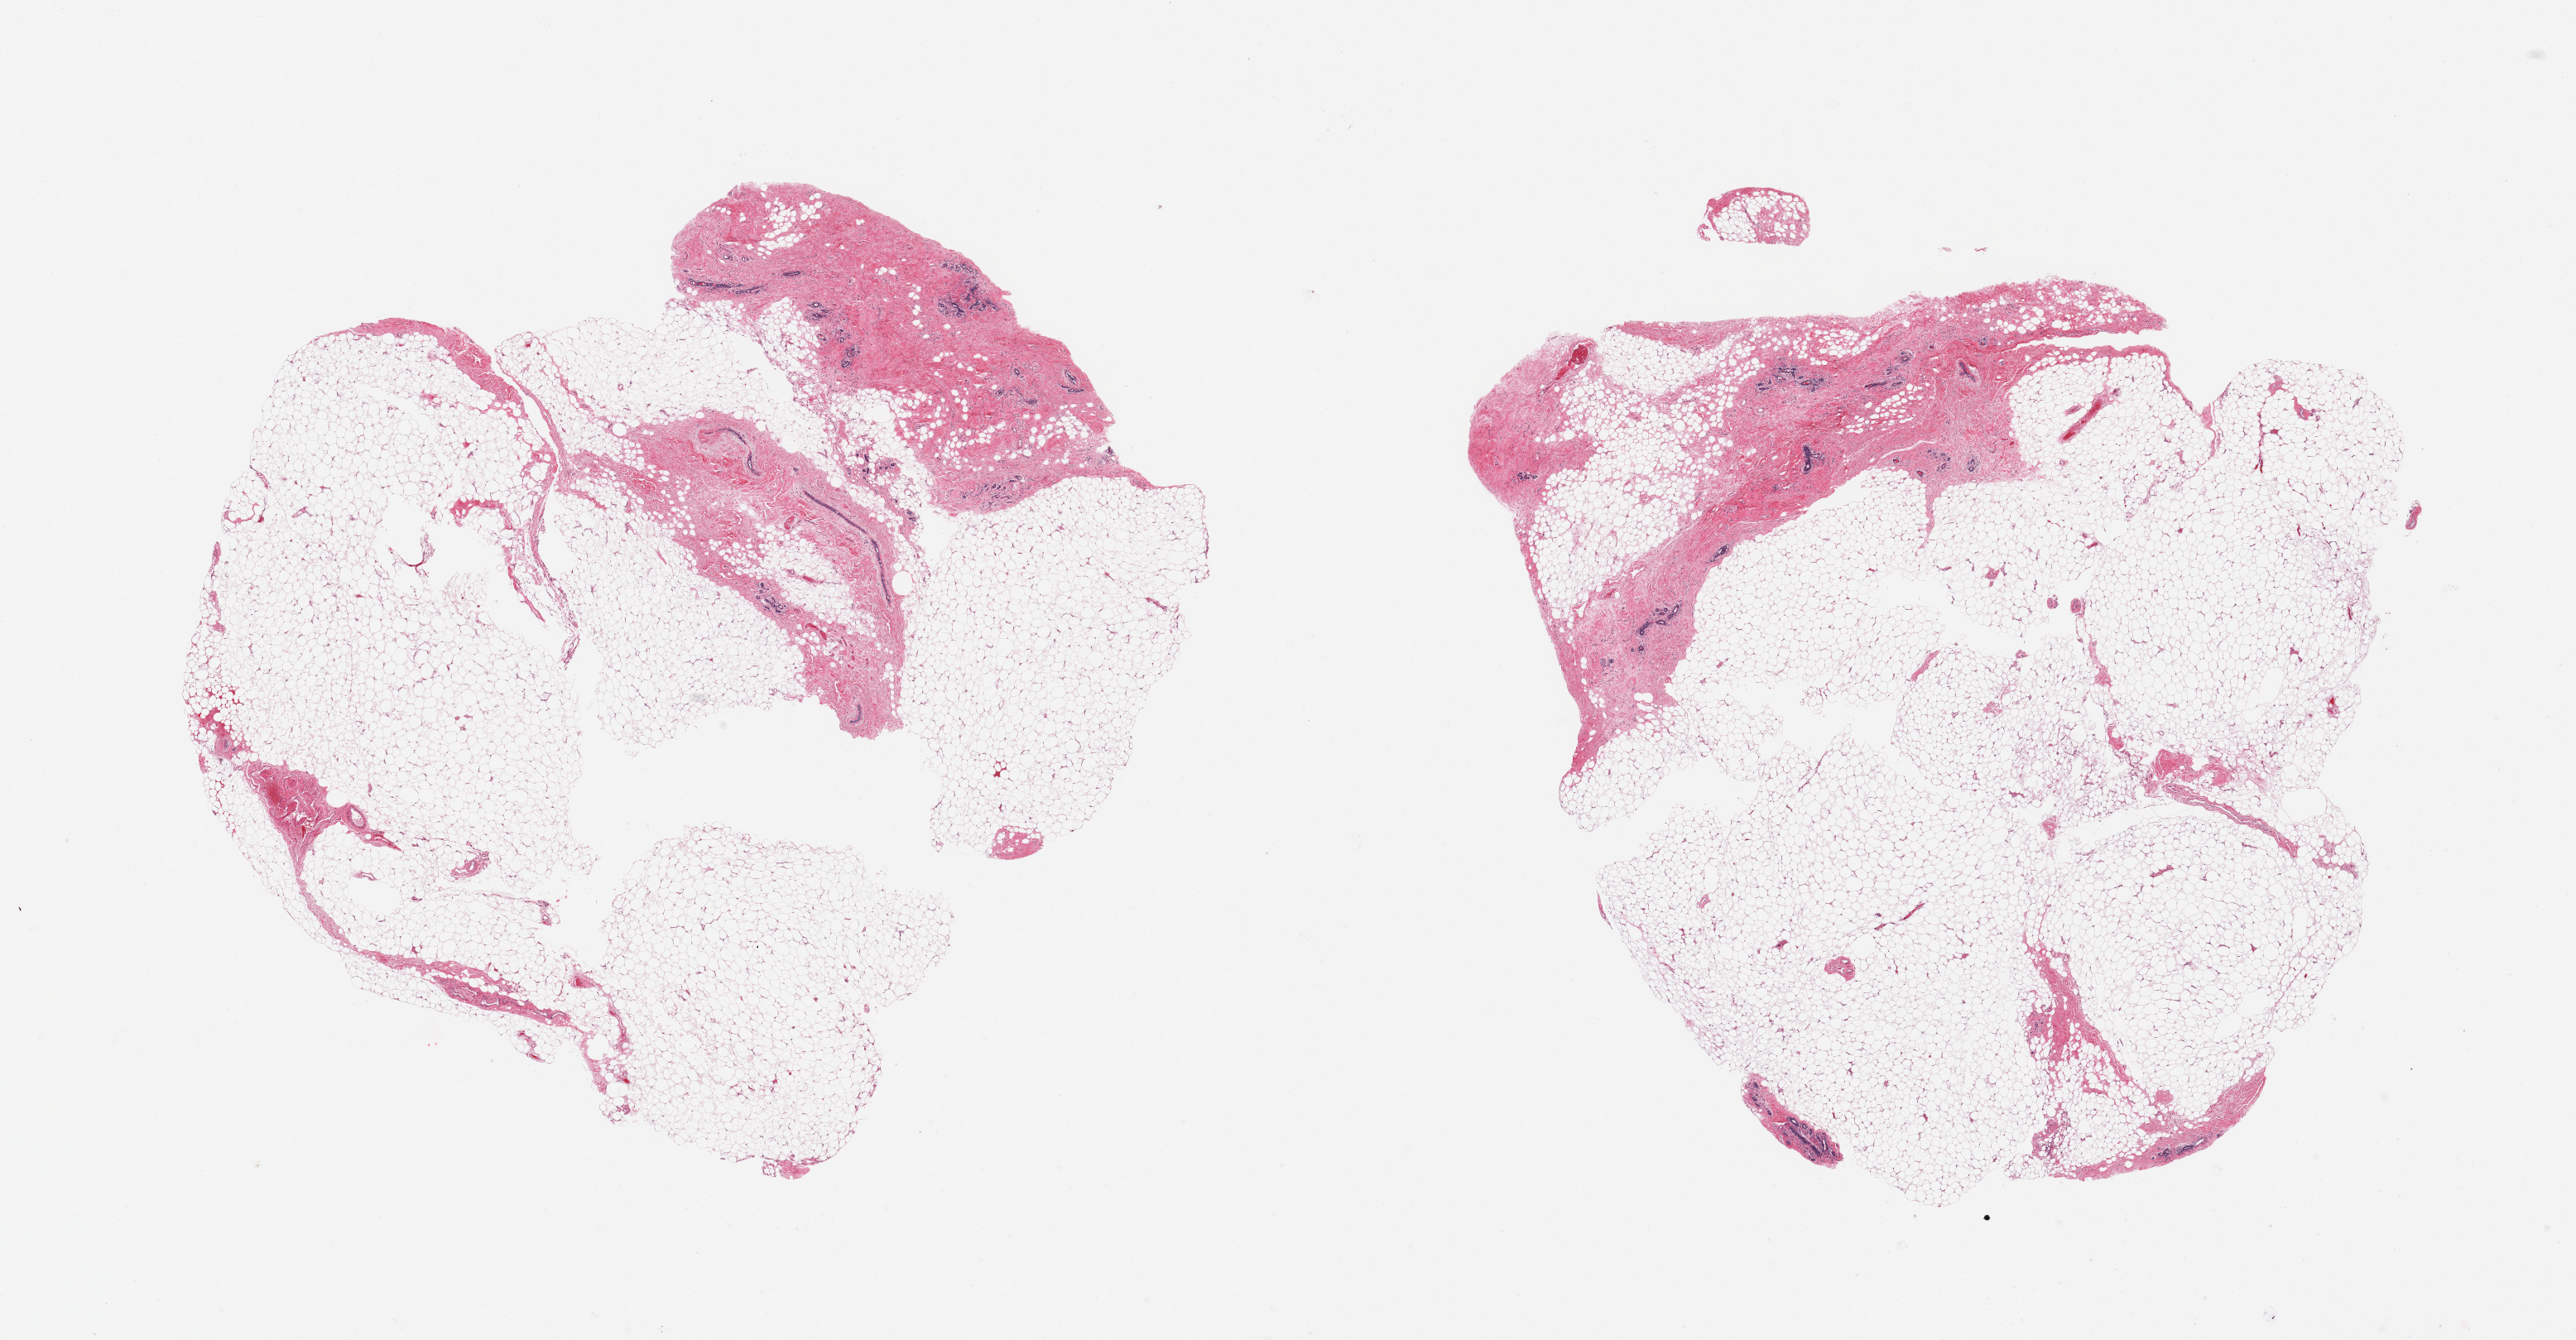
Digitized haematoxylin and eosin-stained section — shown as a low-resolution overview of the whole scanned area (about 24.6 x 12.8 mm, slide scanned at 20x). PAXgene-fixed paraffin-embedded (PFPE) section. Sampled site (target tissue): breast. Tissue donor sample. Donor: female.
• reviewer comment on this tissue sample: 2 pieces; ~80% fat, rest is fibrous stroma with scattered ductal/lobular component